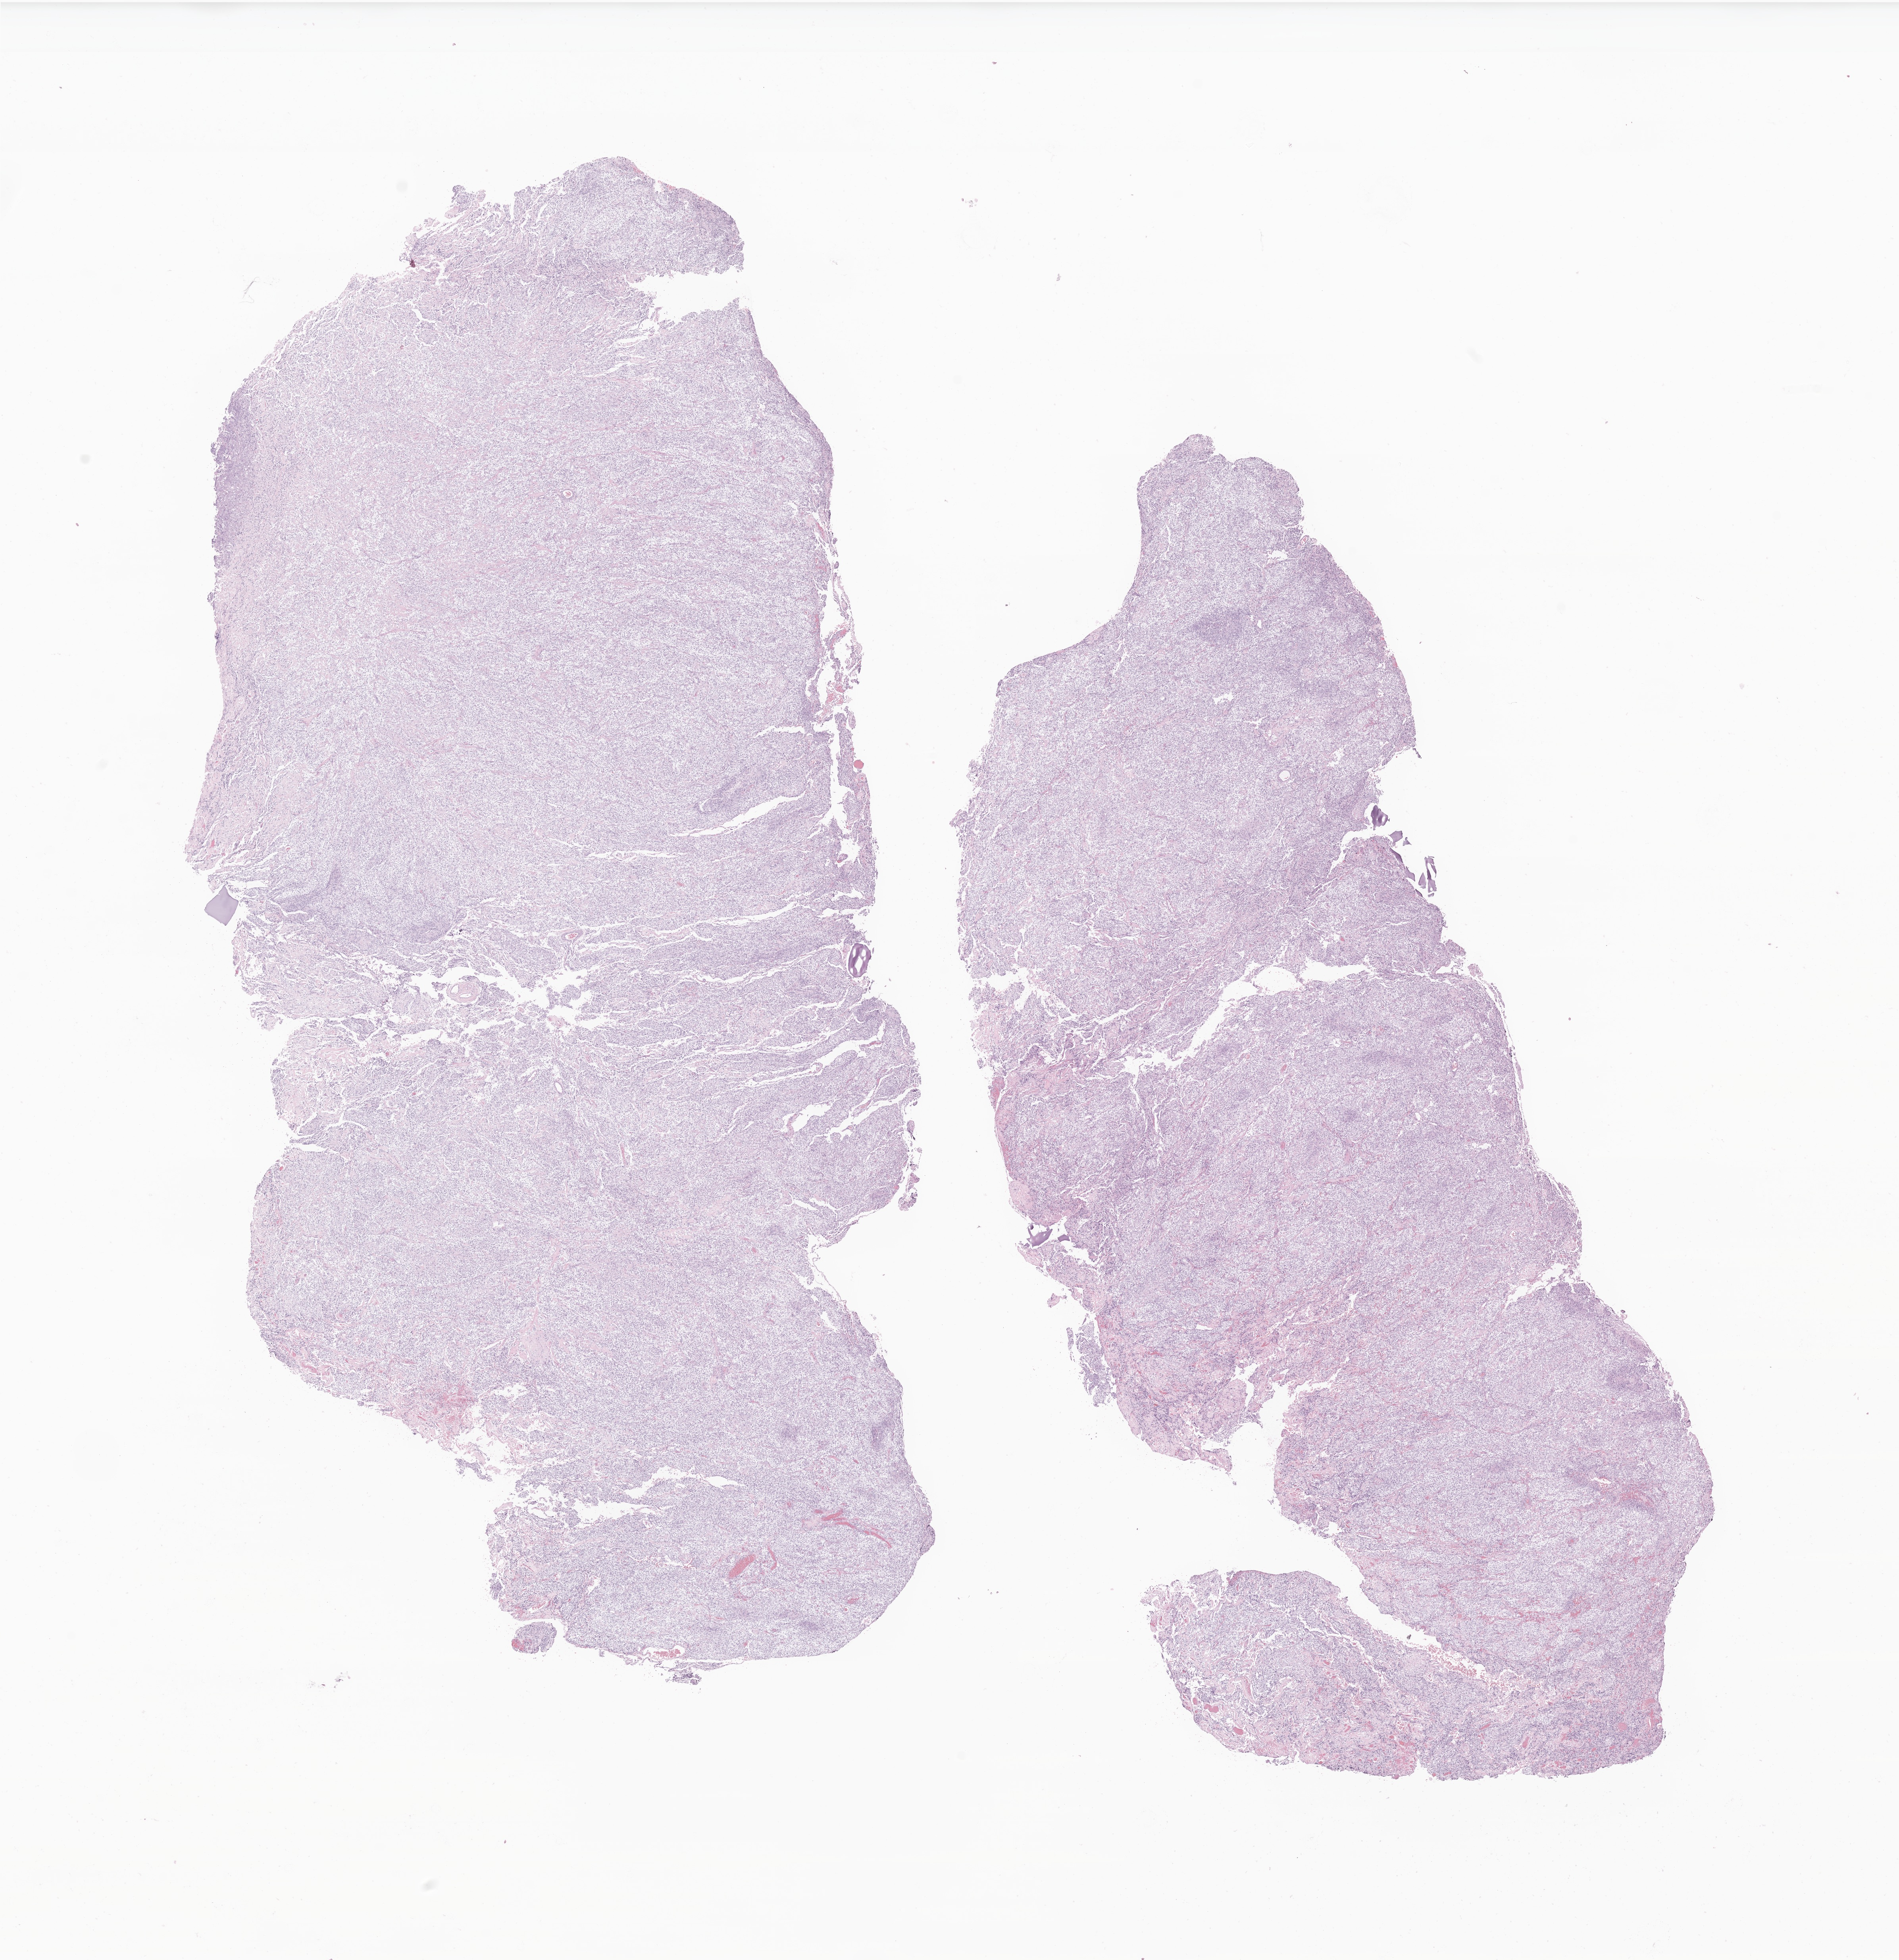
Whole-slide image, haematoxylin and eosin stain of tumor tissue from the brain, low-resolution overview of the scanned area, about 20.2 x 20.8 mm. FFPE section. Female patient, age 147 months (12 years 3 months).
Recorded diagnosis: Neoplasm, uncertain whether benign or malignant.